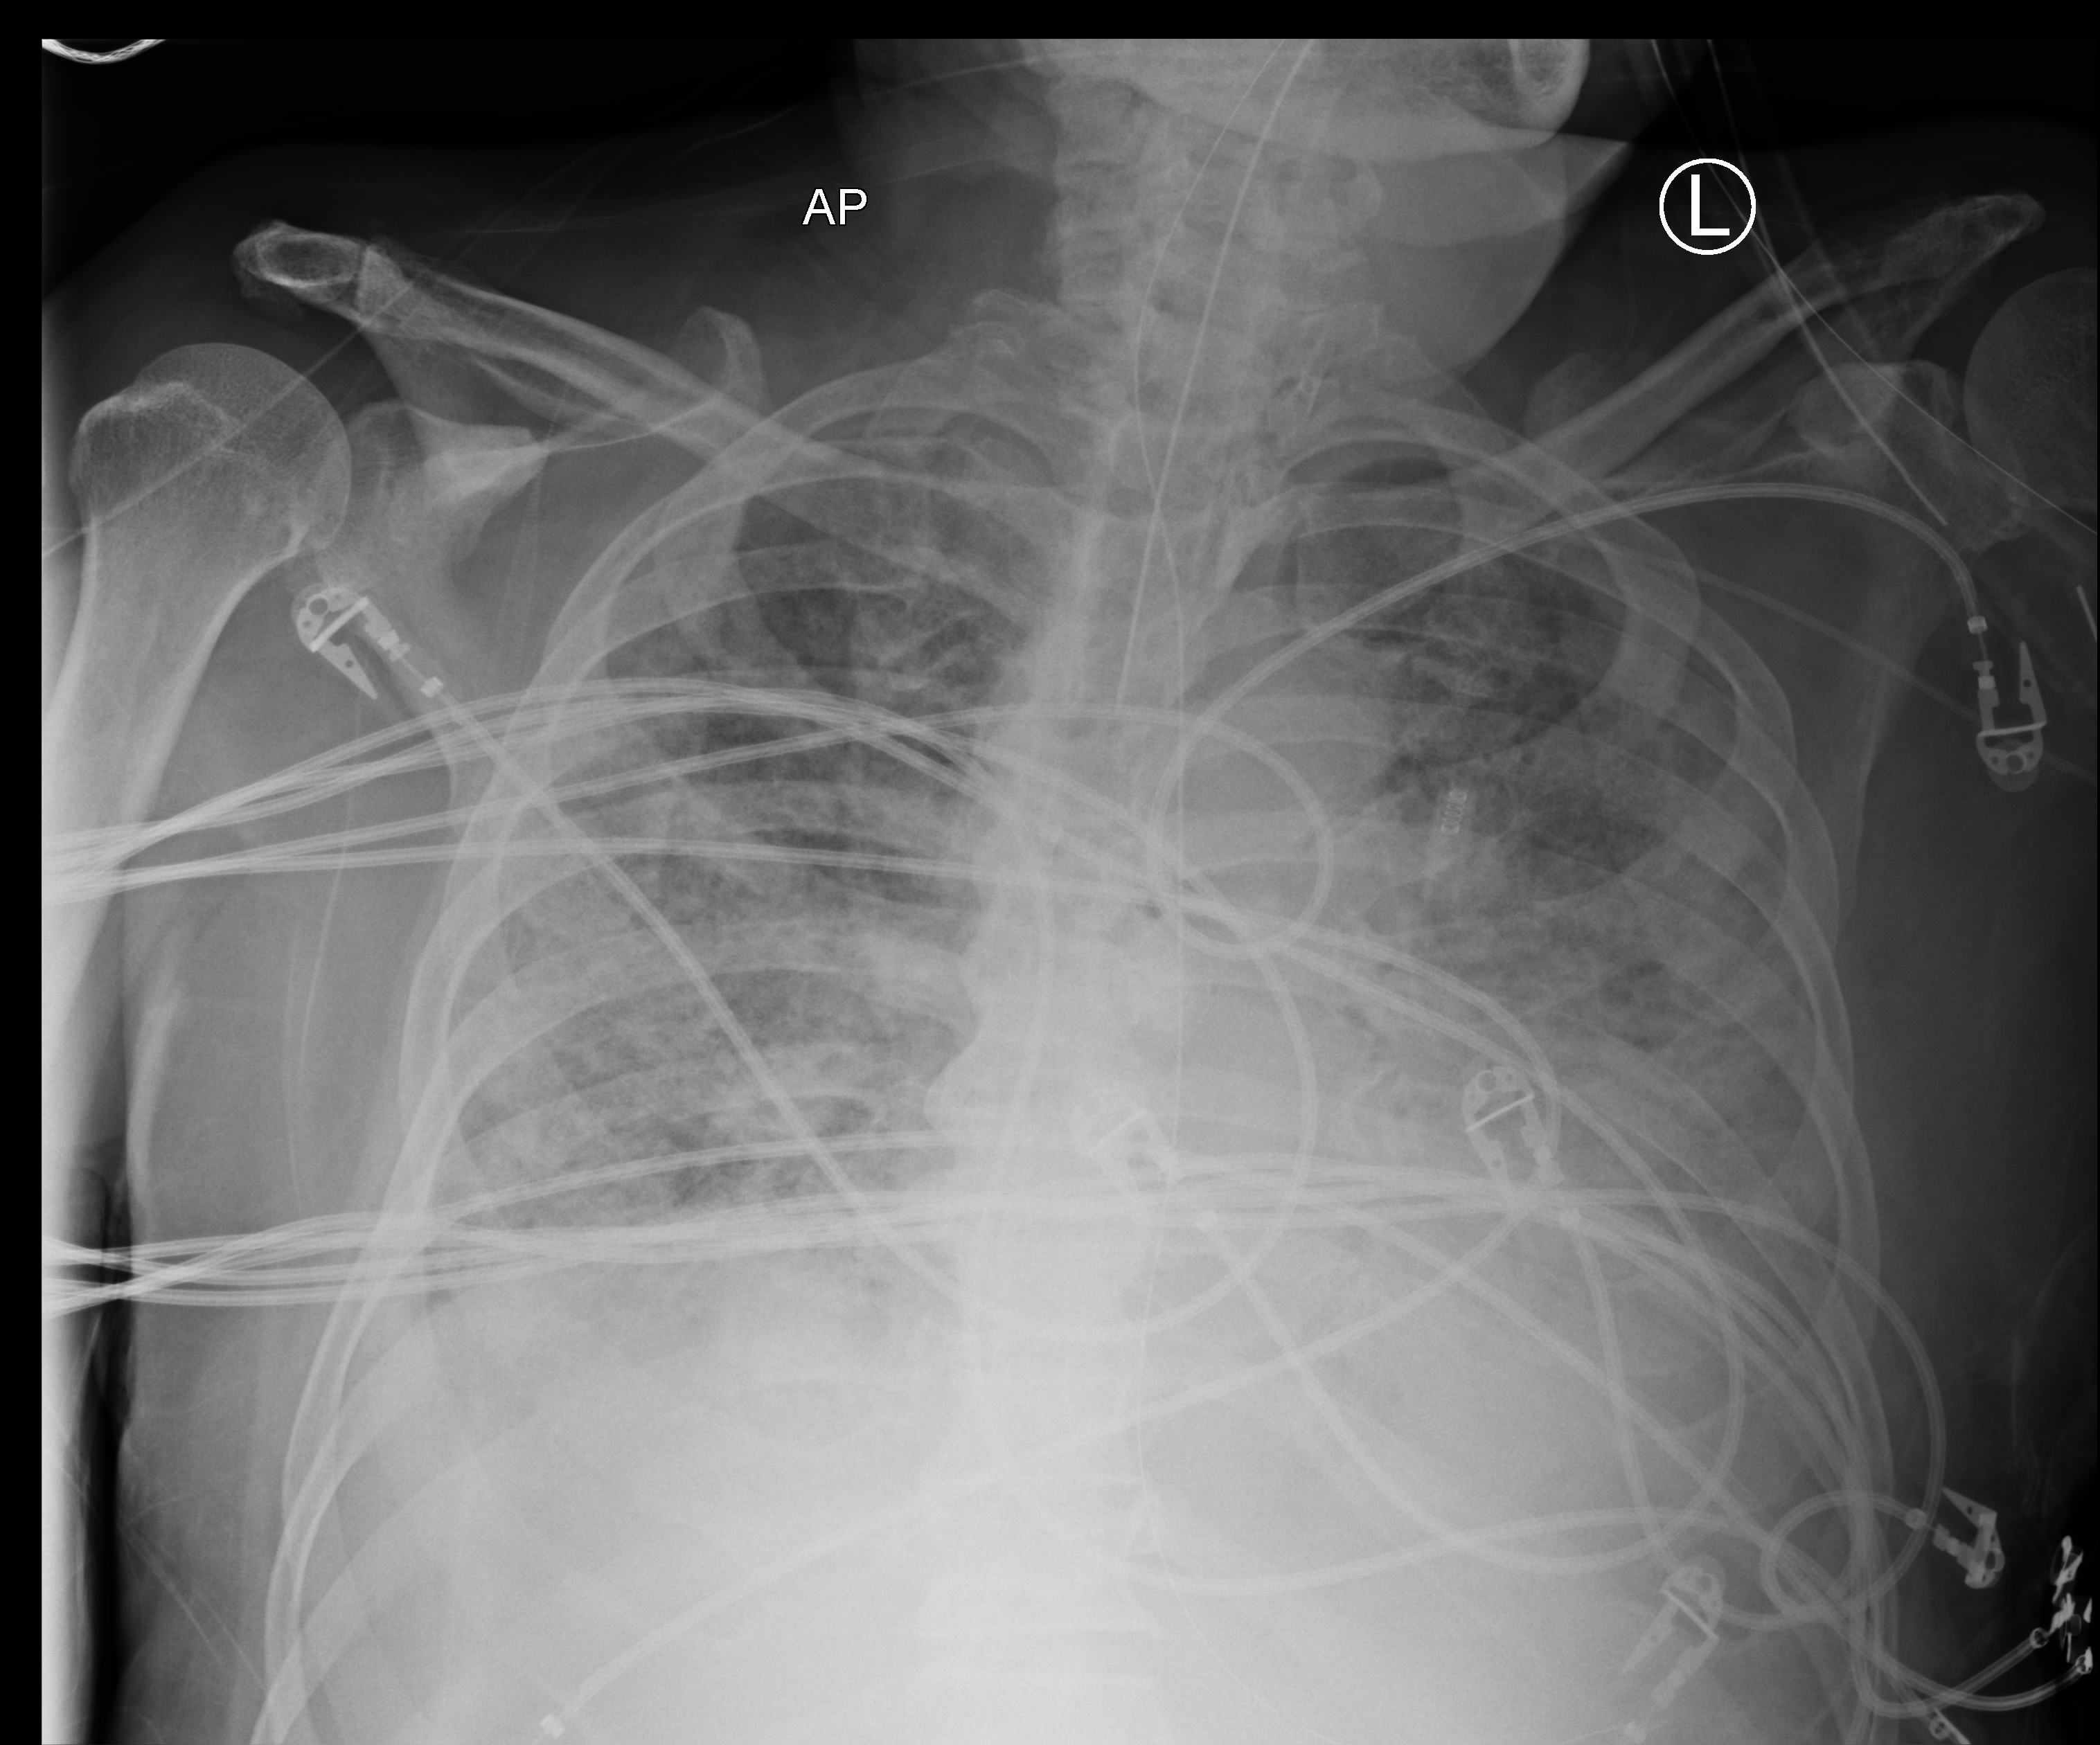
Chest X-ray (portable); anteroposterior (AP) projection. Male patient hospitalised with COVID-19, age 75–90 years.
Admission-level facts for this patient (not findings on this image; timing relative to this image not recorded): length of hospital stay: 33 days.